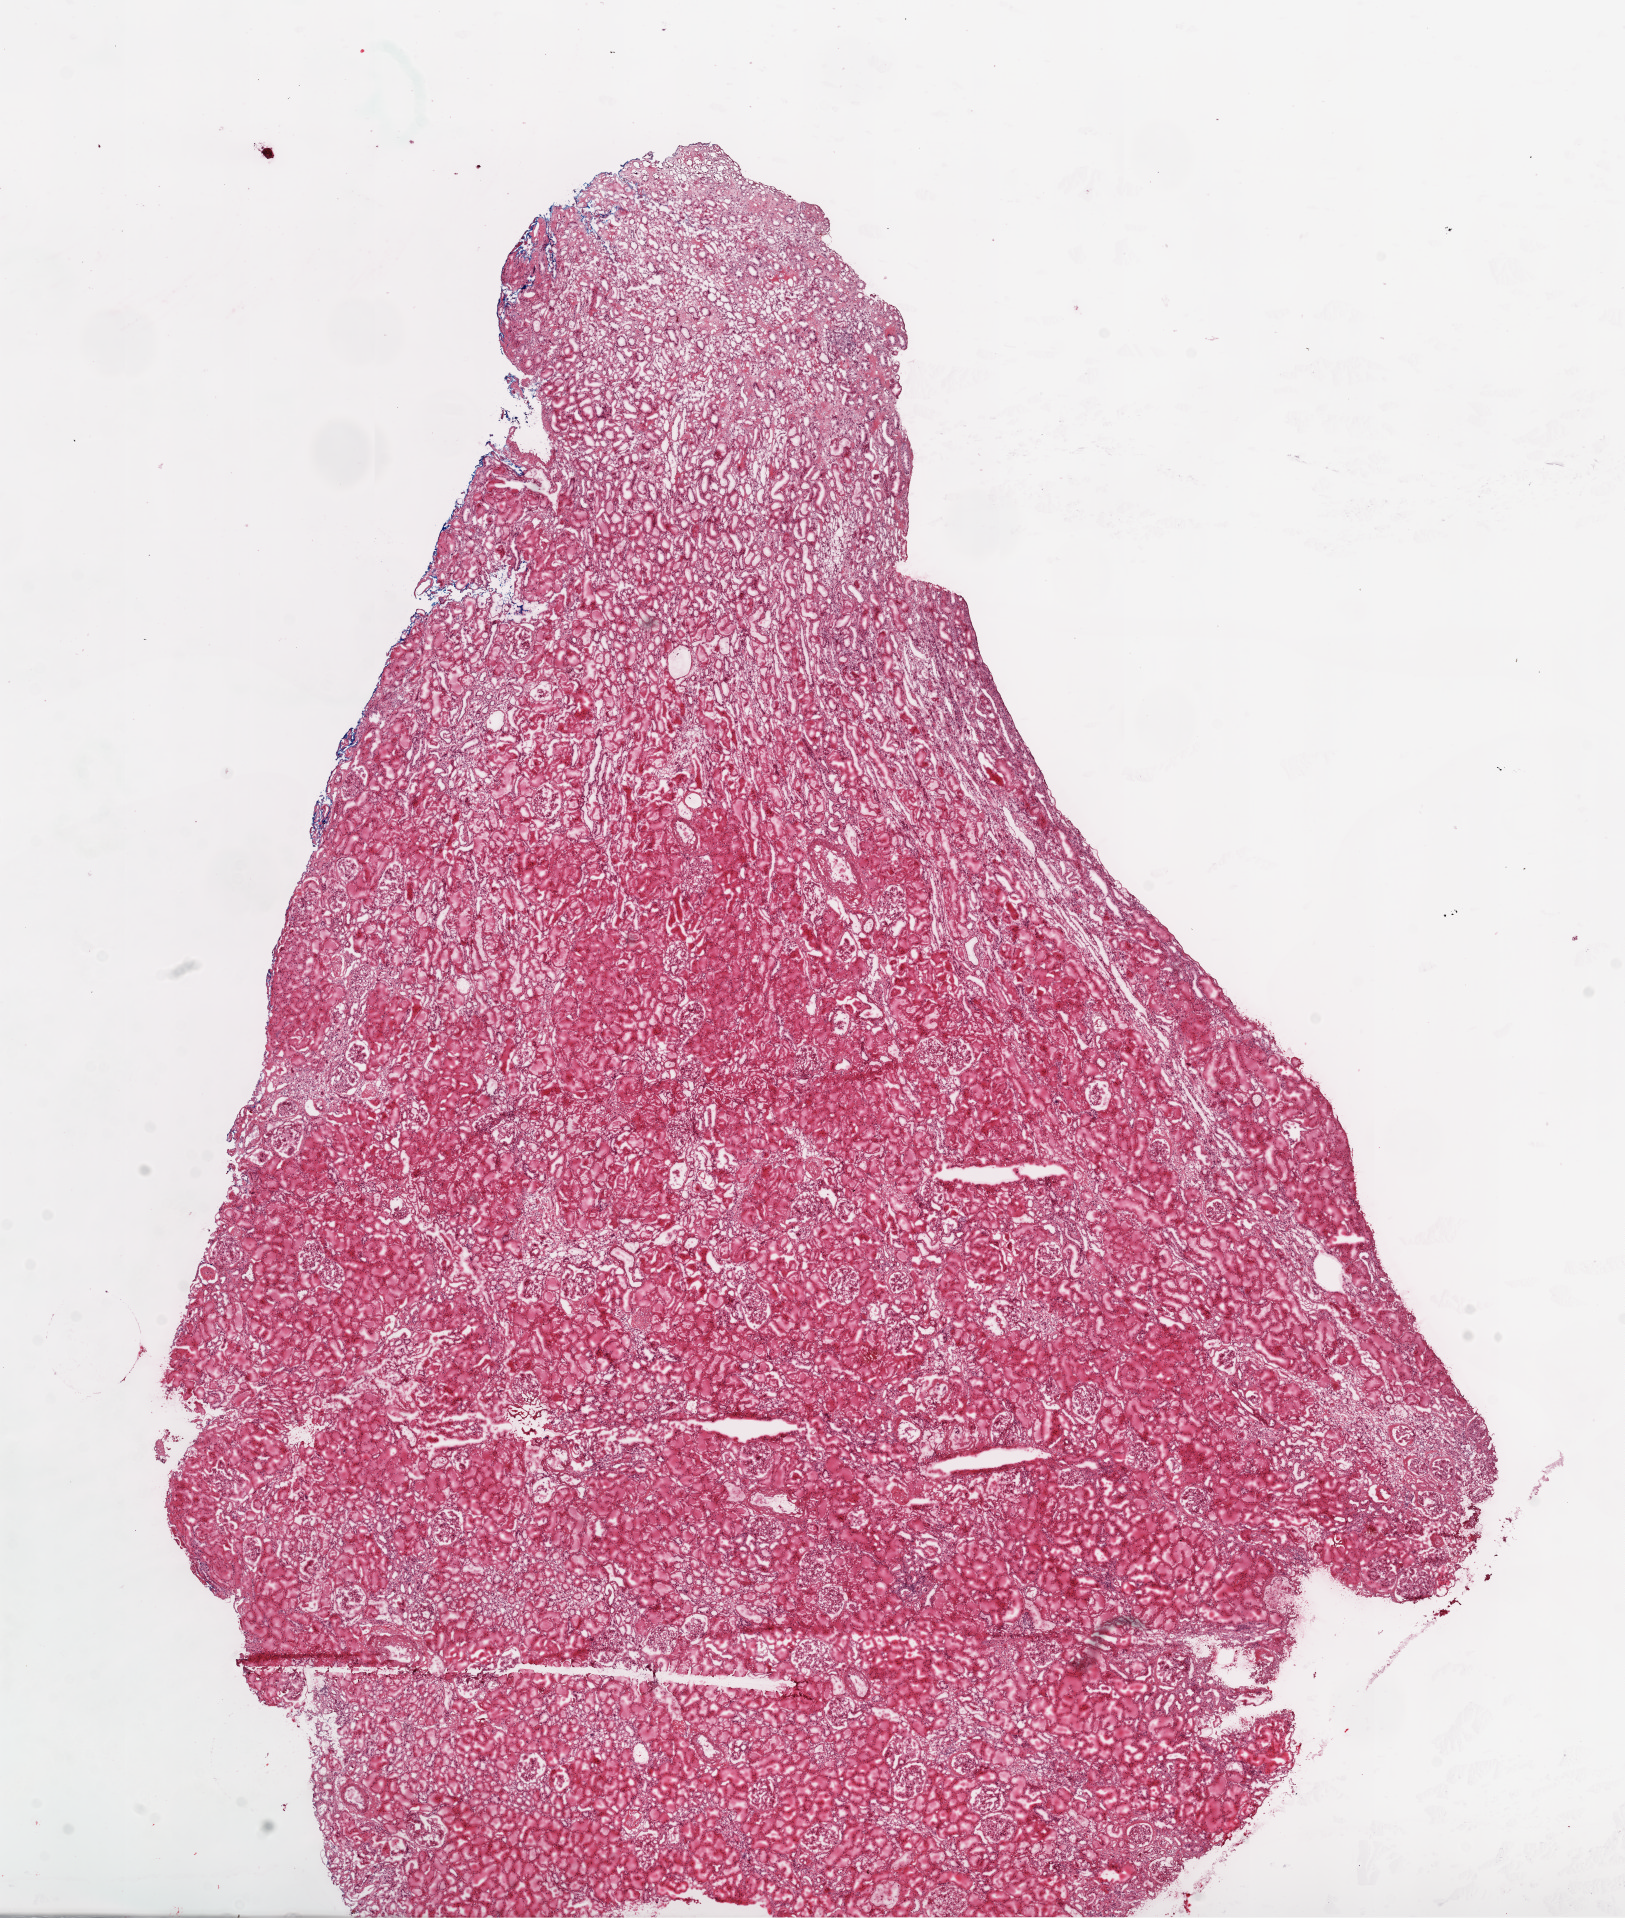
Hematoxylin and eosin (H&E) stained whole-slide image, a low-resolution overview of the entire scanned area, about 13.0 x 15.4 mm. Frozen section from the top of the tissue portion. Kidney, solid tissue normal (non-tumour tissue) sample. Male, age 63 years at initial diagnosis.
This section: solid tissue normal sample (biorepository sample class). Patient diagnosis: Clear cell adenocarcinoma, NOS.